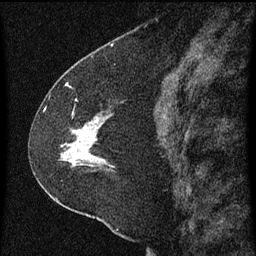
Breast MRI (dynamic contrast-enhanced), one sagittal slice; position 32 of 60 along the scan axis; dynamic contrast-enhanced series, image 2 of 3 at this slice position (ordered by acquisition); 1.5 T; TE 4.2 ms, TR 8 ms; 256 × 256 image matrix. Female patient, age 47 years.
Outlined on this slice (semi-automatic segmentation, software-assisted and operator-edited):
- analysis volume of interest (the breast-tissue region the enhancement analysis was run in; not a lesion): bounding box <36,96,117,213> (left, top, right, bottom; pixels)
- tumour enhancement mask (voxels above the 70 % enhancement threshold inside the analysis volume of interest): <61,120,98,167>